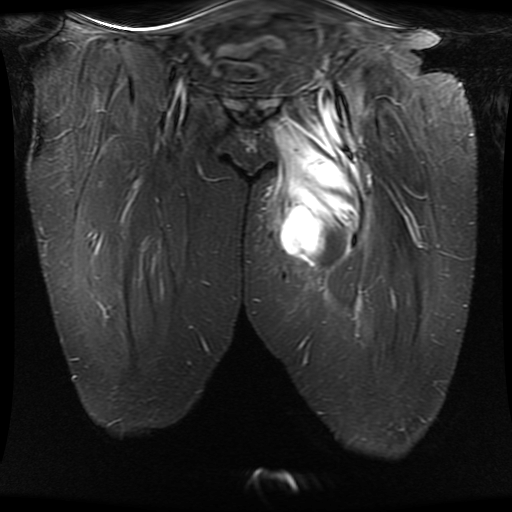
MRI of an extremity soft-tissue mass, one coronal slice. Position 7 of 30 along the scan axis. STIR. 512 × 512 image matrix, field of view 460 × 460 mm. Female patient. From the clinical record (not read from this slice): histological type: myxofibrosarcoma; grade: intermediate; site of the primary tumour: left thigh.
Structures marked on this image (manually delineated by an expert):
- gross tumour volume including surrounding oedema: bounding box (x1, y1, x2, y2) in pixels: (272, 88, 372, 269)
- gross tumour volume (mass): (280, 158, 359, 266)